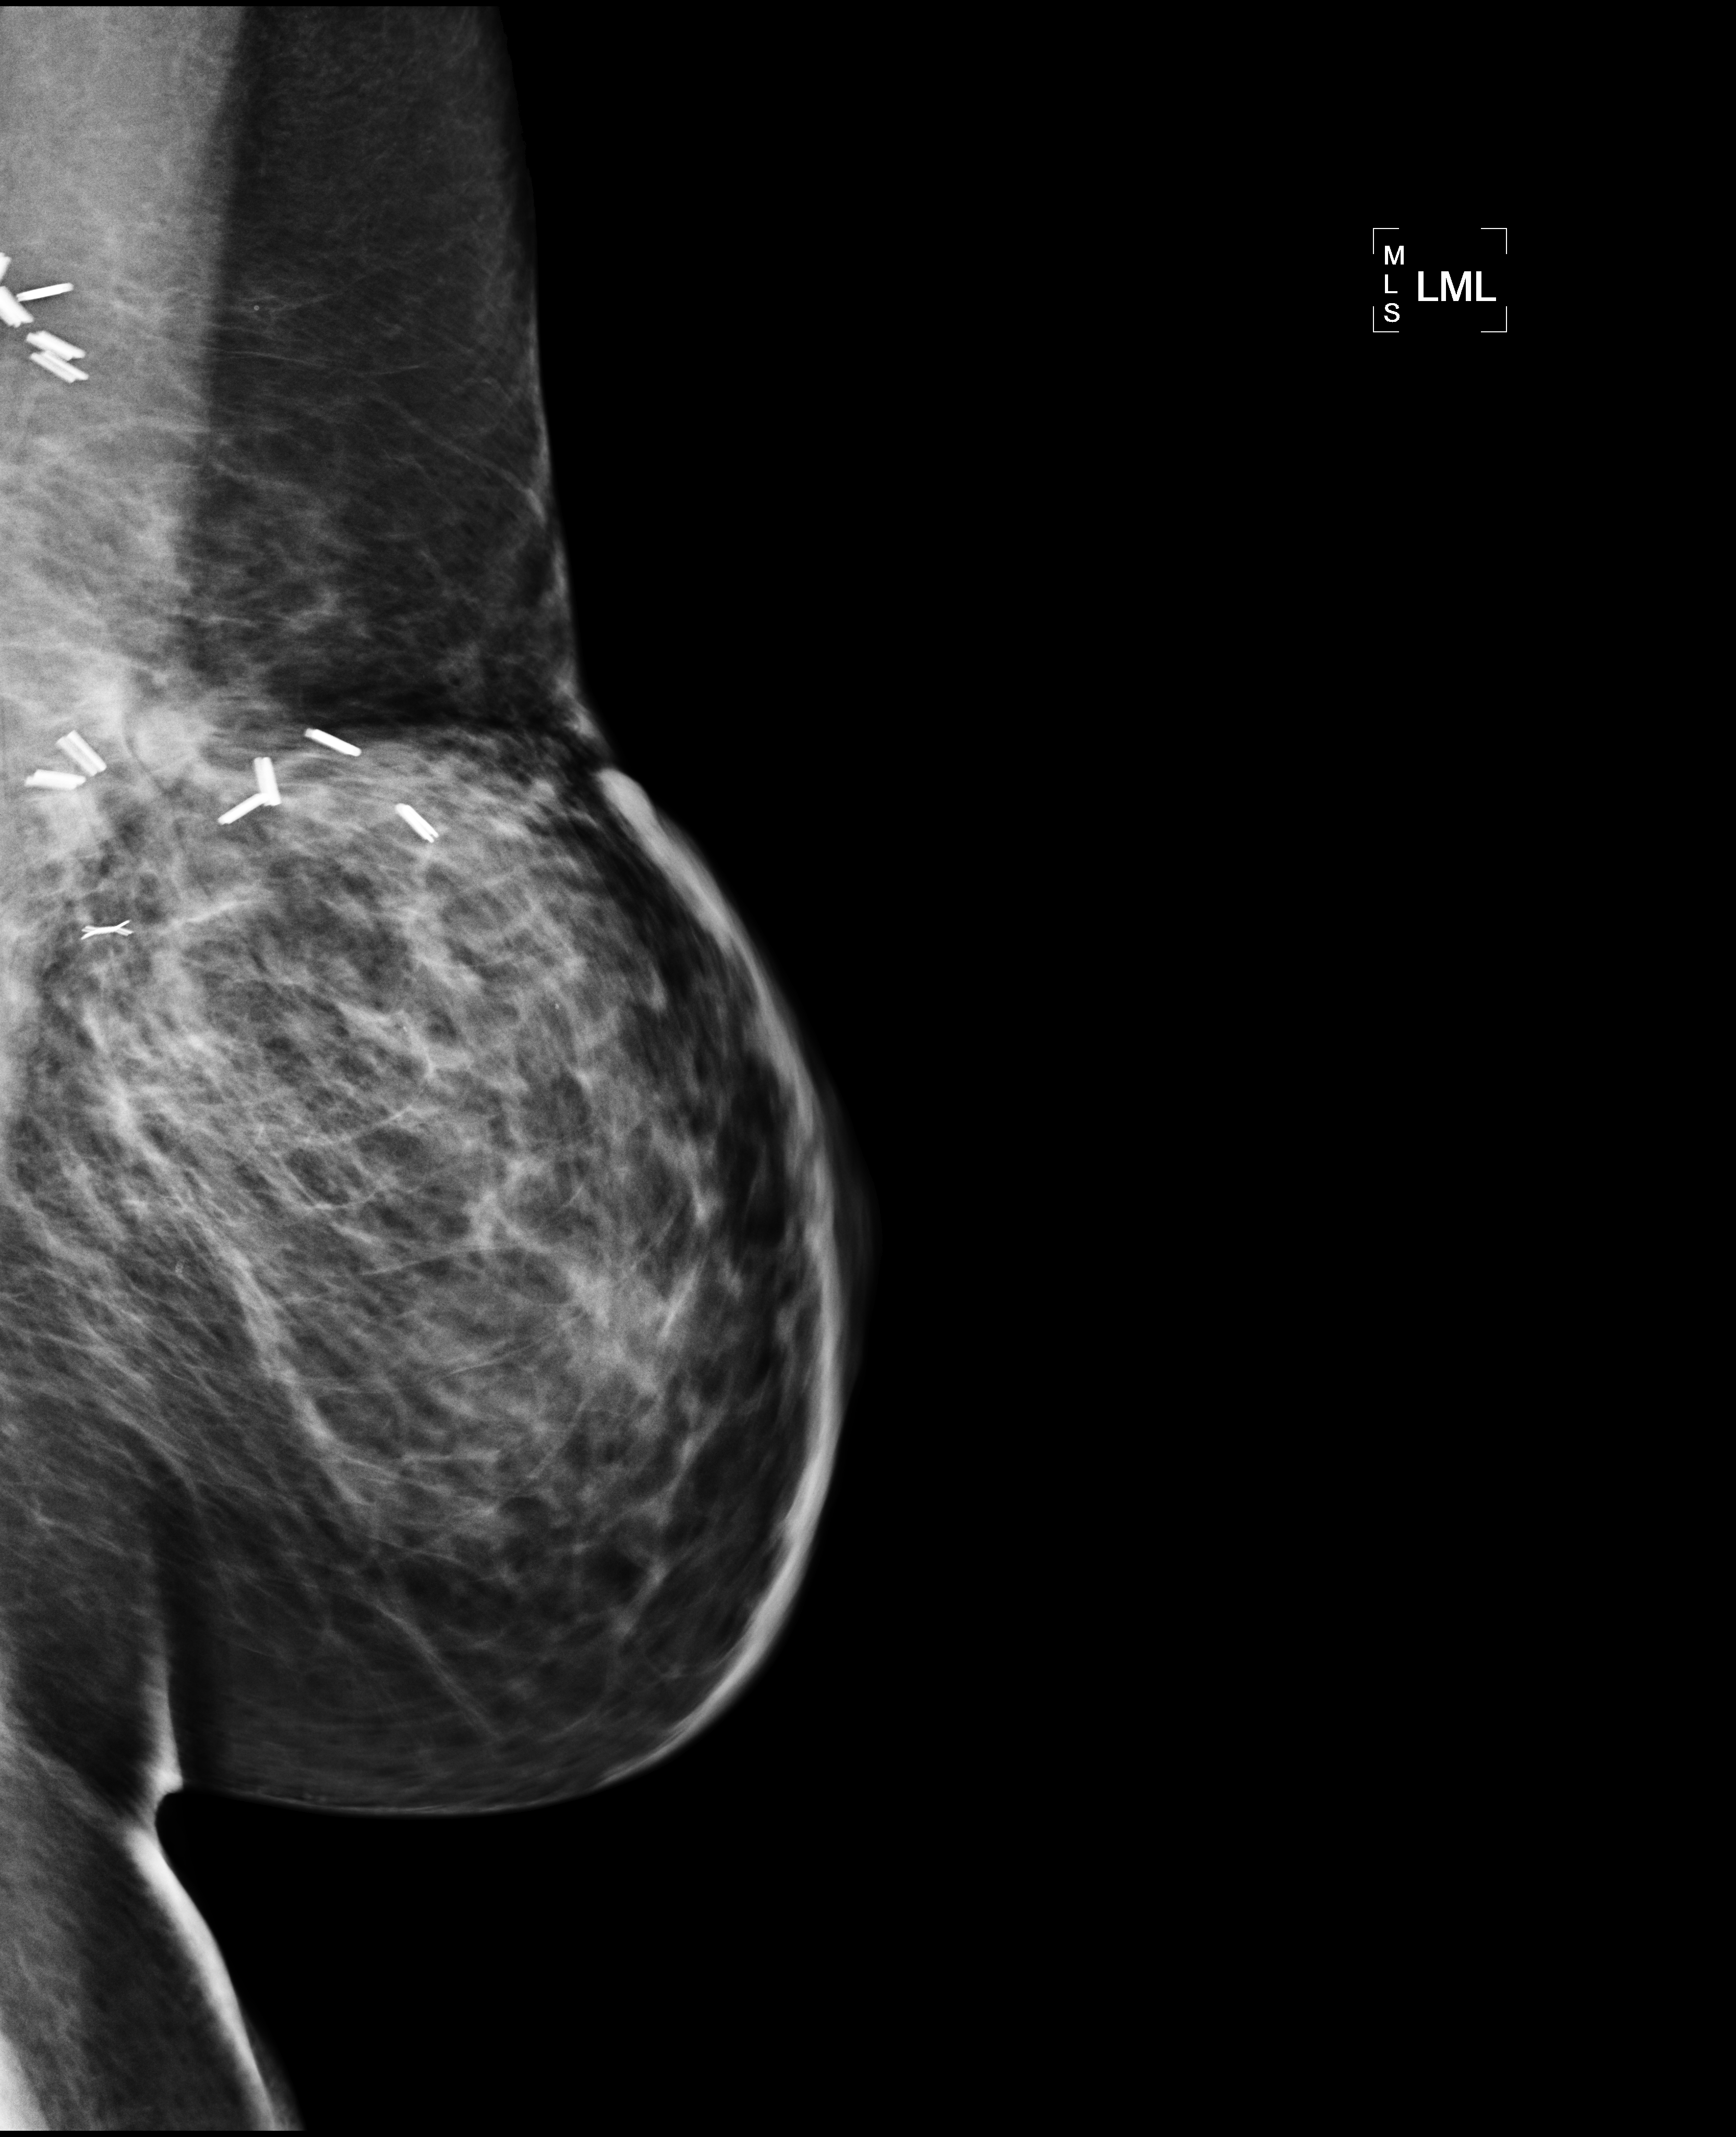
Mammogram, left breast, ML view; patient in her 50s.
Patient-level pathology facts (clinical record, not image findings): pathology diagnosis: Invasive ductal CA (left breast); receptor status (as recorded): ER pos, PR pos (weak), HER2 neg; Ki-67 (as recorded): intermed prolif; pathology report notes: re-bx [date] was scar tissue from RT rx.